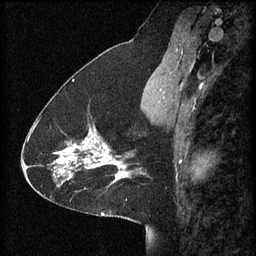
Breast MRI (dynamic contrast-enhanced), one sagittal slice. Position 28 of 60 along the scan axis. 3 images stored at this slice position (order not interpretable as contrast timing). 1.5 T. TE 4.2 ms, TR 8.2 ms. 2 mm slice thickness. 256 × 256 image matrix. Patient: female, 41 years.
Annotated regions visible in this slice (semi-automatic segmentation, software-assisted and operator-edited):
- analysis volume of interest (the breast-tissue region the enhancement analysis was run in; not a lesion): bounding box [x1, y1, x2, y2] px = [58, 116, 128, 181]
- tumour enhancement mask (voxels above the 70 % enhancement threshold inside the analysis volume of interest): [58, 128, 128, 181]